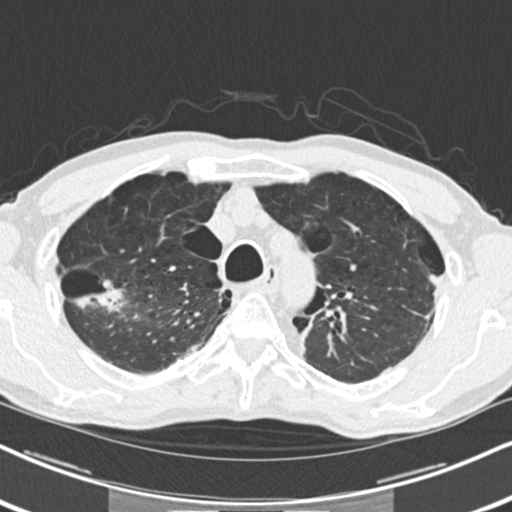
Axial slice from a low-dose chest CT screening exam; first (baseline) screen; lung window (W 1500 / L -600 HU); 2 mm slice thickness; standard (soft-tissue) reconstruction kernel (B30f); slice 53 of 250 in the series. Male, age 71 years at enrolment. Current smoker at enrolment.
- Expert reader's lesion annotation, bounding box <87,269,142,316> (left, top, right, bottom; pixels).
- The screening reader recorded 2 non-calcified nodules or masses ≥4 mm on this exam; which of them this box marks is not recorded.
- Official screen result: positive, change unspecified: nodule(s) >= 4 mm or enlarging nodule(s), mass(es), or other non-specific abnormalities suspicious for lung cancer.
- Participant outcome: lung cancer diagnosed 454 days after this screen (after the second annual screen) — adenocarcinoma, NOS, right upper lobe, well differentiated (G1), stage IA (AJCC 6th edition), 30 mm at pathology.